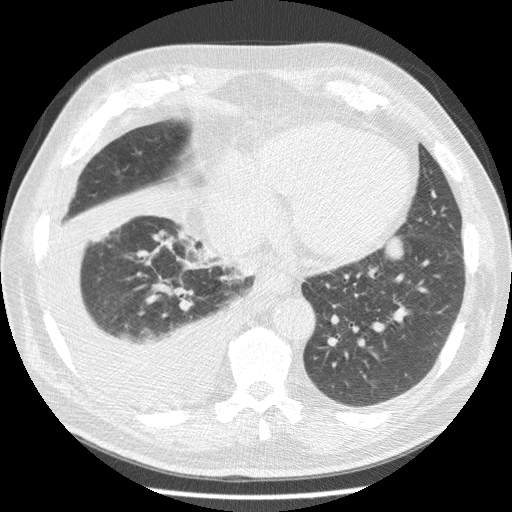
Low-dose screening chest CT, one axial slice. Position 64 of 180 along the scan axis. Reconstruction kernel STANDARD. Lung window (W 1500 / L -600 HU). 512 × 512 image matrix, field of view 355 × 355 mm.
Structures marked on this image (outlined manually by an expert reader):
- lesion 1 (tumor, lower lobe of left lung): bounding box [x1, y1, x2, y2] px = [385, 237, 403, 259]